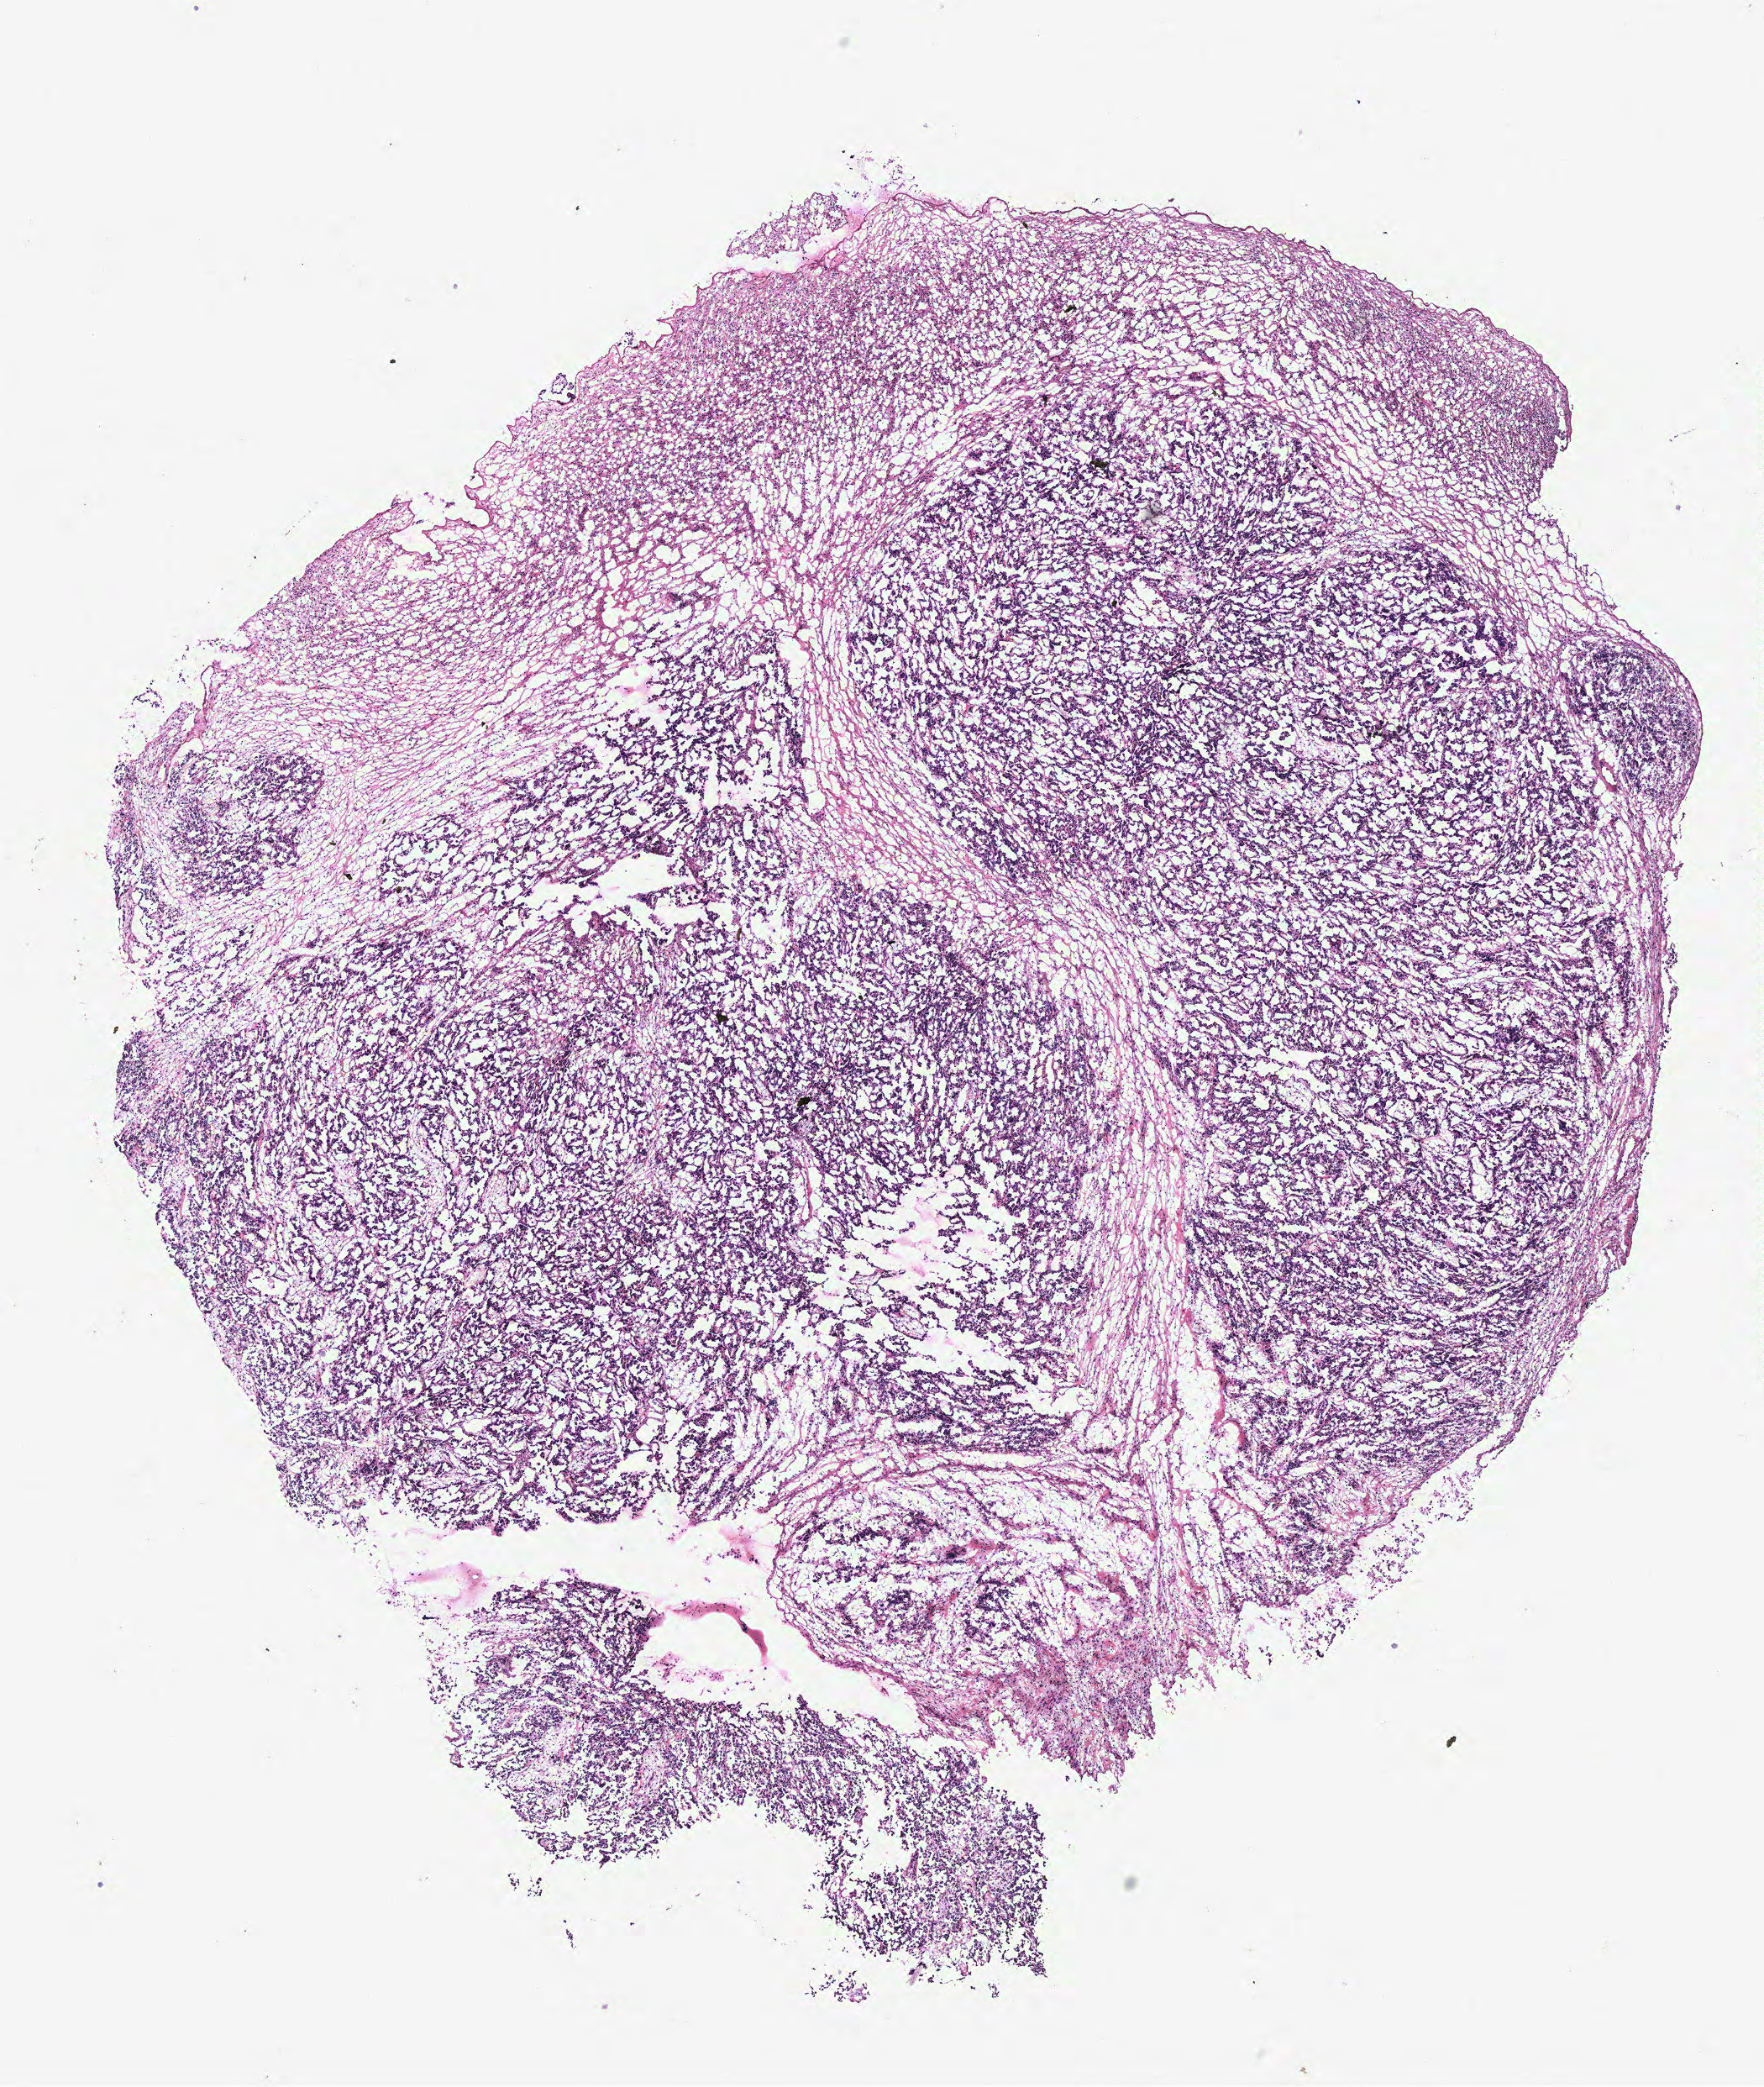
Hematoxylin and eosin (H&E) stained whole-slide image, whole scanned area (about 8.4 x 9.9 mm) shown as a low-resolution overview. Tumour tissue sample, ovary. Patient: female, age 74 years.
Primary tumour site (as recorded): peritoneum. Diagnosis: Serous adenocarcinoma, NOS.